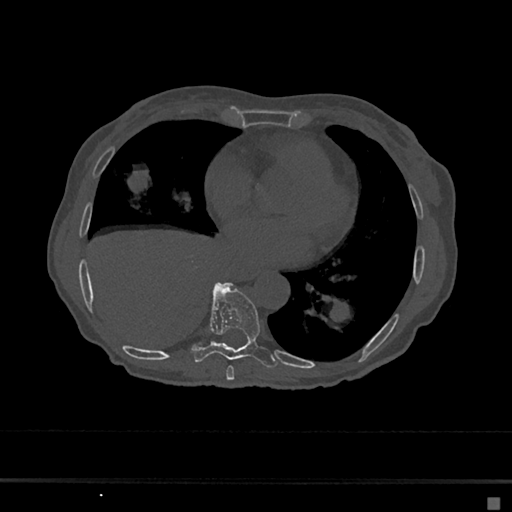
CT including the spine, one axial slice. 120 kVp. Bone window (W 1800 / L 400 HU). 512 × 512 image matrix. Female patient, age 68 years. Case-level facts recorded for this patient, not image findings: primary cancer: renal.
Annotated regions visible in this slice (semi-automatic segmentation, software-assisted and operator-edited):
- T7 vertebra: box from (x=226, y=366) to (x=235, y=381) px
- T8 vertebra: (x=192, y=282)–(x=277, y=368)